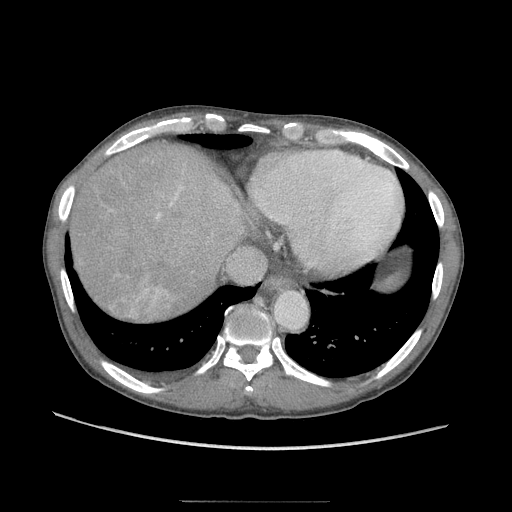
Contrast-enhanced abdominal CT (liver protocol), one axial slice. Slice 86 of 103 in the series (ordered by position). Reconstruction kernel STANDARD. 120 kVp. Soft-tissue window (W 400 / L 40 HU). 512 × 512 image matrix. Case-level facts recorded for this patient, not image findings: diagnosis: hepatocellular carcinoma (patient treated with transarterial chemoembolisation; whether this scan precedes or follows treatment is not stated here); TNM stage (as recorded): Stage-IIIA; Child-Pugh class: A; tumour nodularity: multinodular; tumour size: 16 cm.
Annotated regions visible in this slice (semi-automatically segmented with operator editing):
- abdominal aorta: bounding box [x1, y1, x2, y2] px = [275, 292, 307, 328]
- liver parenchyma outside the tumour (the mass and vessels are separate outlines, so this box may not span the whole liver): [72, 140, 236, 312]
- mass: [112, 293, 132, 313]